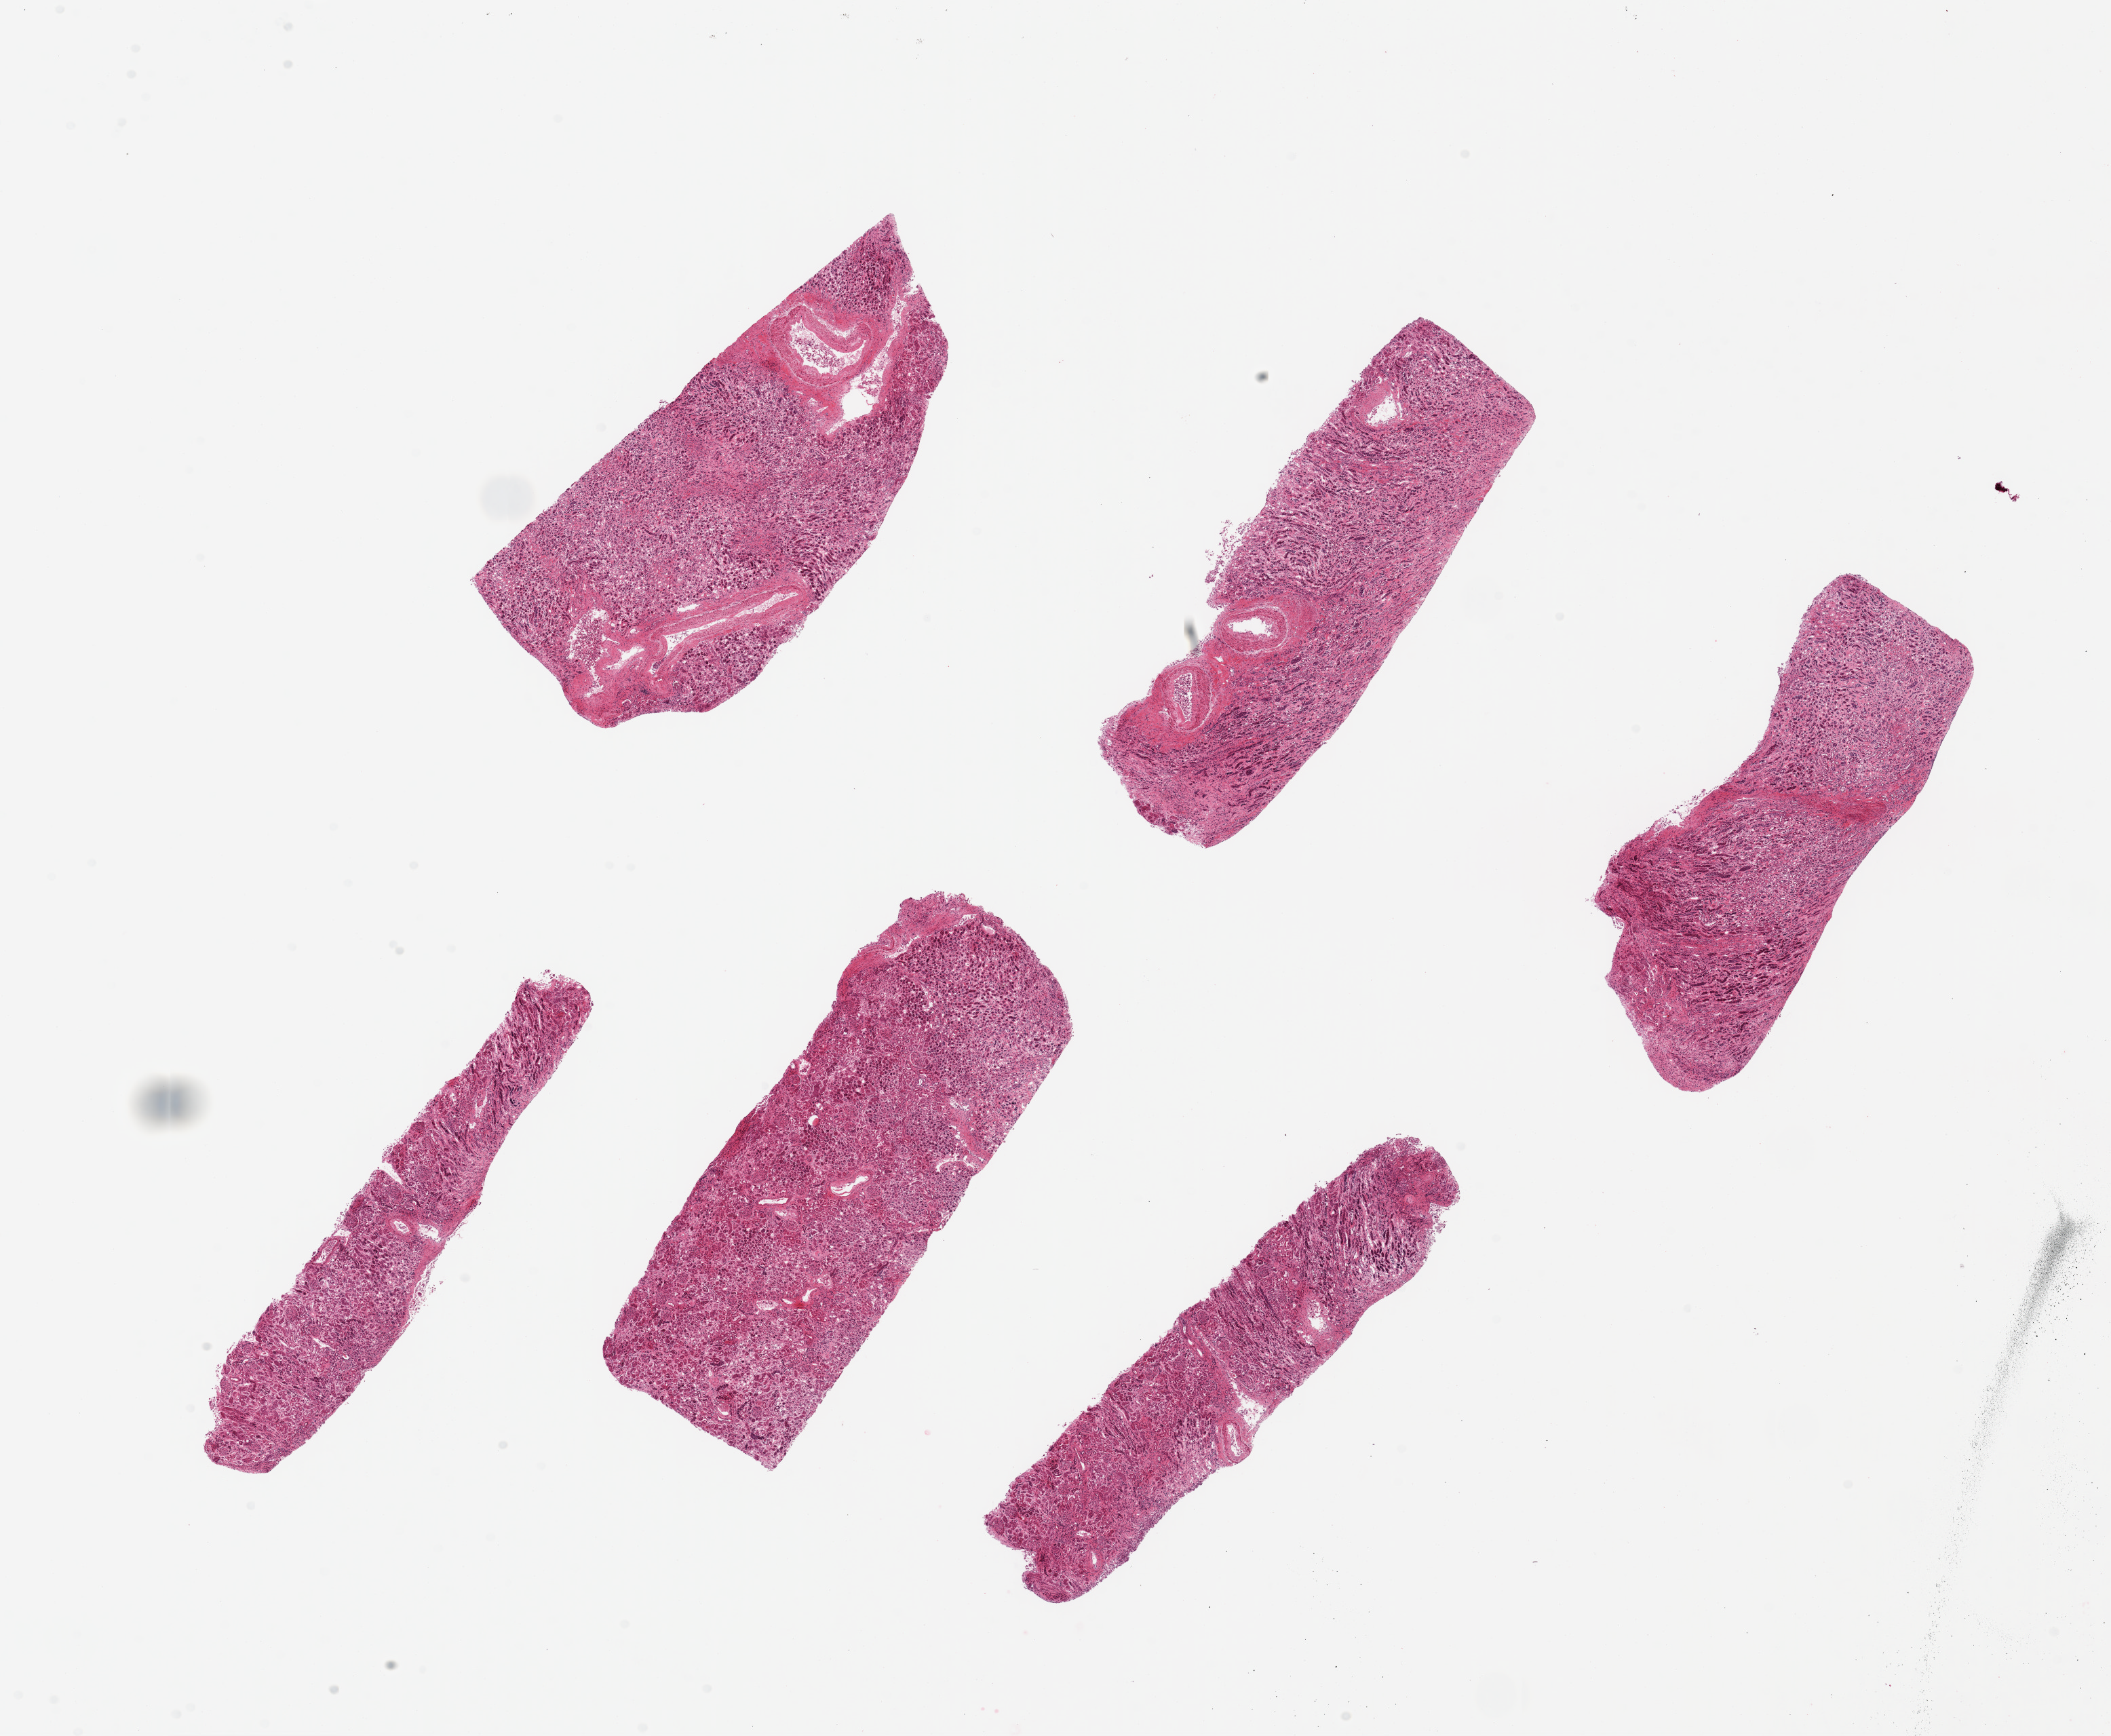
Digitized hematoxylin and eosin (H&E)-stained section, a low-resolution overview of the entire scanned area, about 24.6 x 20.2 mm (slide scanned at 20x), PAXgene-fixed, paraffin-embedded tissue, sampled site (target tissue): renal cortex, tissue donor sample.
Pathologist's review note for this sample: 6 pieces 3 with some glomeruli, 3 largely medulla ~6x2mm.